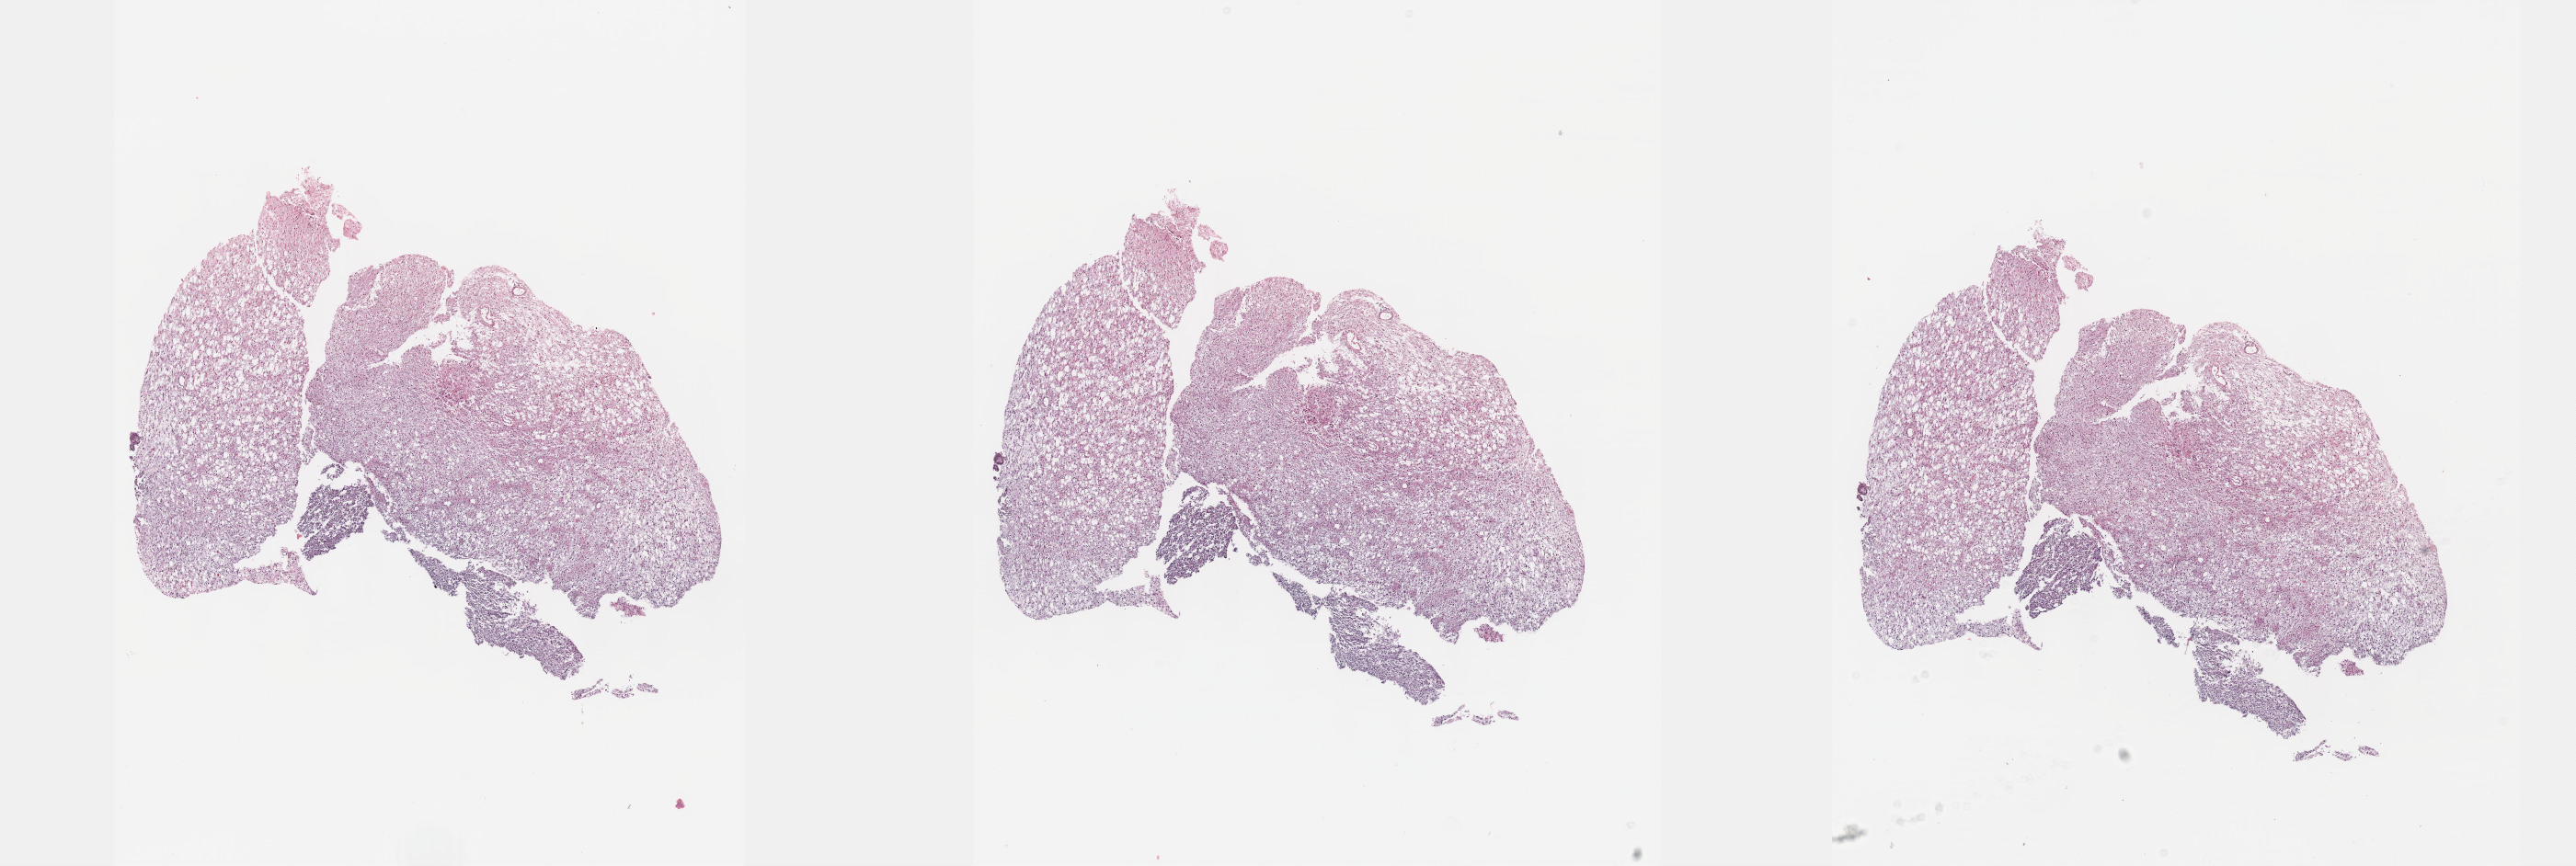
Digitized H&E tissue section (whole slide), a low-resolution overview of the entire scanned area, about 22.6 x 7.6 mm, formalin-fixed paraffin-embedded (FFPE) diagnostic section, primary tumour sample from the brain. Male patient; age at initial diagnosis 53 years. Histologic grade: G2 (moderately differentiated).
Pathologic diagnosis: Oligodendroglioma, NOS (cerebrum).